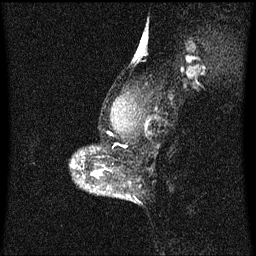
Breast MRI (dynamic contrast-enhanced), one sagittal slice. Slice 48 of 60 in the series (ordered by position). Dynamic contrast-enhanced series, image 2 of 3 at this slice position (ordered by acquisition). 1.5 T. TE 4.2 ms, TR 8.4 ms. 2 mm slice thickness. 256 × 256 image matrix, field of view 200 × 200 mm. Female patient, age 40 years.
Annotated regions visible in this slice (semi-automatically segmented with operator editing):
- analysis volume of interest (the breast-tissue region the enhancement analysis was run in; not a lesion): bounding box [x1, y1, x2, y2] px = [93, 172, 103, 177]
- tumour enhancement mask (voxels above the 70 % enhancement threshold inside the analysis volume of interest): [93, 172, 101, 177]